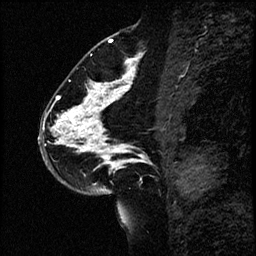
Breast MRI (dynamic contrast-enhanced), one sagittal slice; slice 35 of 60 in the series (ordered by position); dynamic contrast-enhanced study with each time point stored as its own series, time point 2 of 4 at this slice position (early post-contrast, ordered by acquisition time); 1.5 T; TE 4.2 ms, TR 17.6 ms; 2 mm slice thickness; 256 × 256 image matrix, field of view 200 × 200 mm. Patient: female, 43 years. Case-level facts recorded for this patient, not image findings: setting: breast cancer imaged before/during neoadjuvant chemotherapy.
Structures marked on this image (semi-automatic segmentation, software-assisted and operator-edited):
- analysis volume of interest (the breast-tissue region the enhancement analysis was run in; not a lesion): box from (x=41, y=56) to (x=169, y=191) px
- tumour enhancement mask (voxels above the 100 % enhancement threshold inside the analysis volume of interest): (x=56, y=56)–(x=145, y=167)